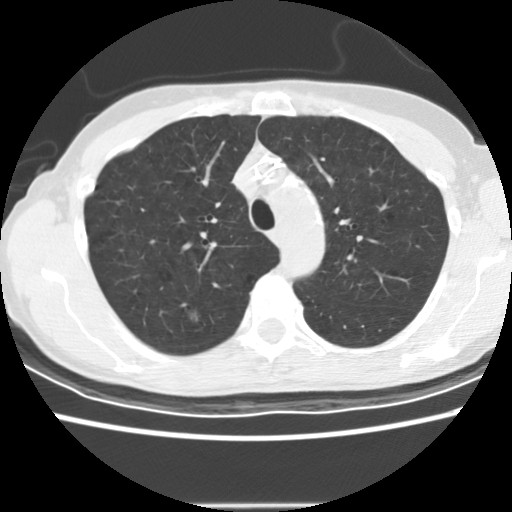
Axial slice from a low-dose chest CT screening exam, second annual screen, lung window (W 1500 / L -600 HU), standard (soft-tissue) reconstruction kernel (STANDARD), slice 40 of 166 in the series. Female participant, aged 58 years at enrolment.
Expert-annotated lung lesion, bounding box [x1, y1, x2, y2] px = [173, 300, 211, 330]. The screening reader recorded 2 non-calcified nodules or masses ≥4 mm on this exam (right upper lobe, right upper lobe); which of them this box marks is not recorded. Official screen result: positive, change unspecified: nodule(s) >= 4 mm or enlarging nodule(s), mass(es), or other non-specific abnormalities suspicious for lung cancer.